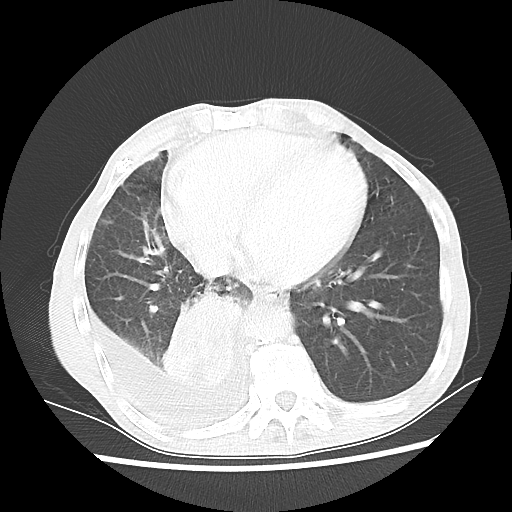
Chest CT, one axial slice. Position 21 of 60 along the scan axis. 80 kVp. Lung window (W 1500 / L -600 HU). 512 × 512 image matrix, field of view 335 × 335 mm. Male patient, age 76 years. Case-level facts recorded for this patient, not image findings: clinical TNM (as recorded): T3 N3 M1a; histopathological grade: G3.
Annotated regions visible in this slice (rectangle marked by the reading radiologist):
- lung tumour (recorded histology: squamous cell carcinoma): bounding box (x1, y1, x2, y2) in pixels: (160, 287, 250, 395)